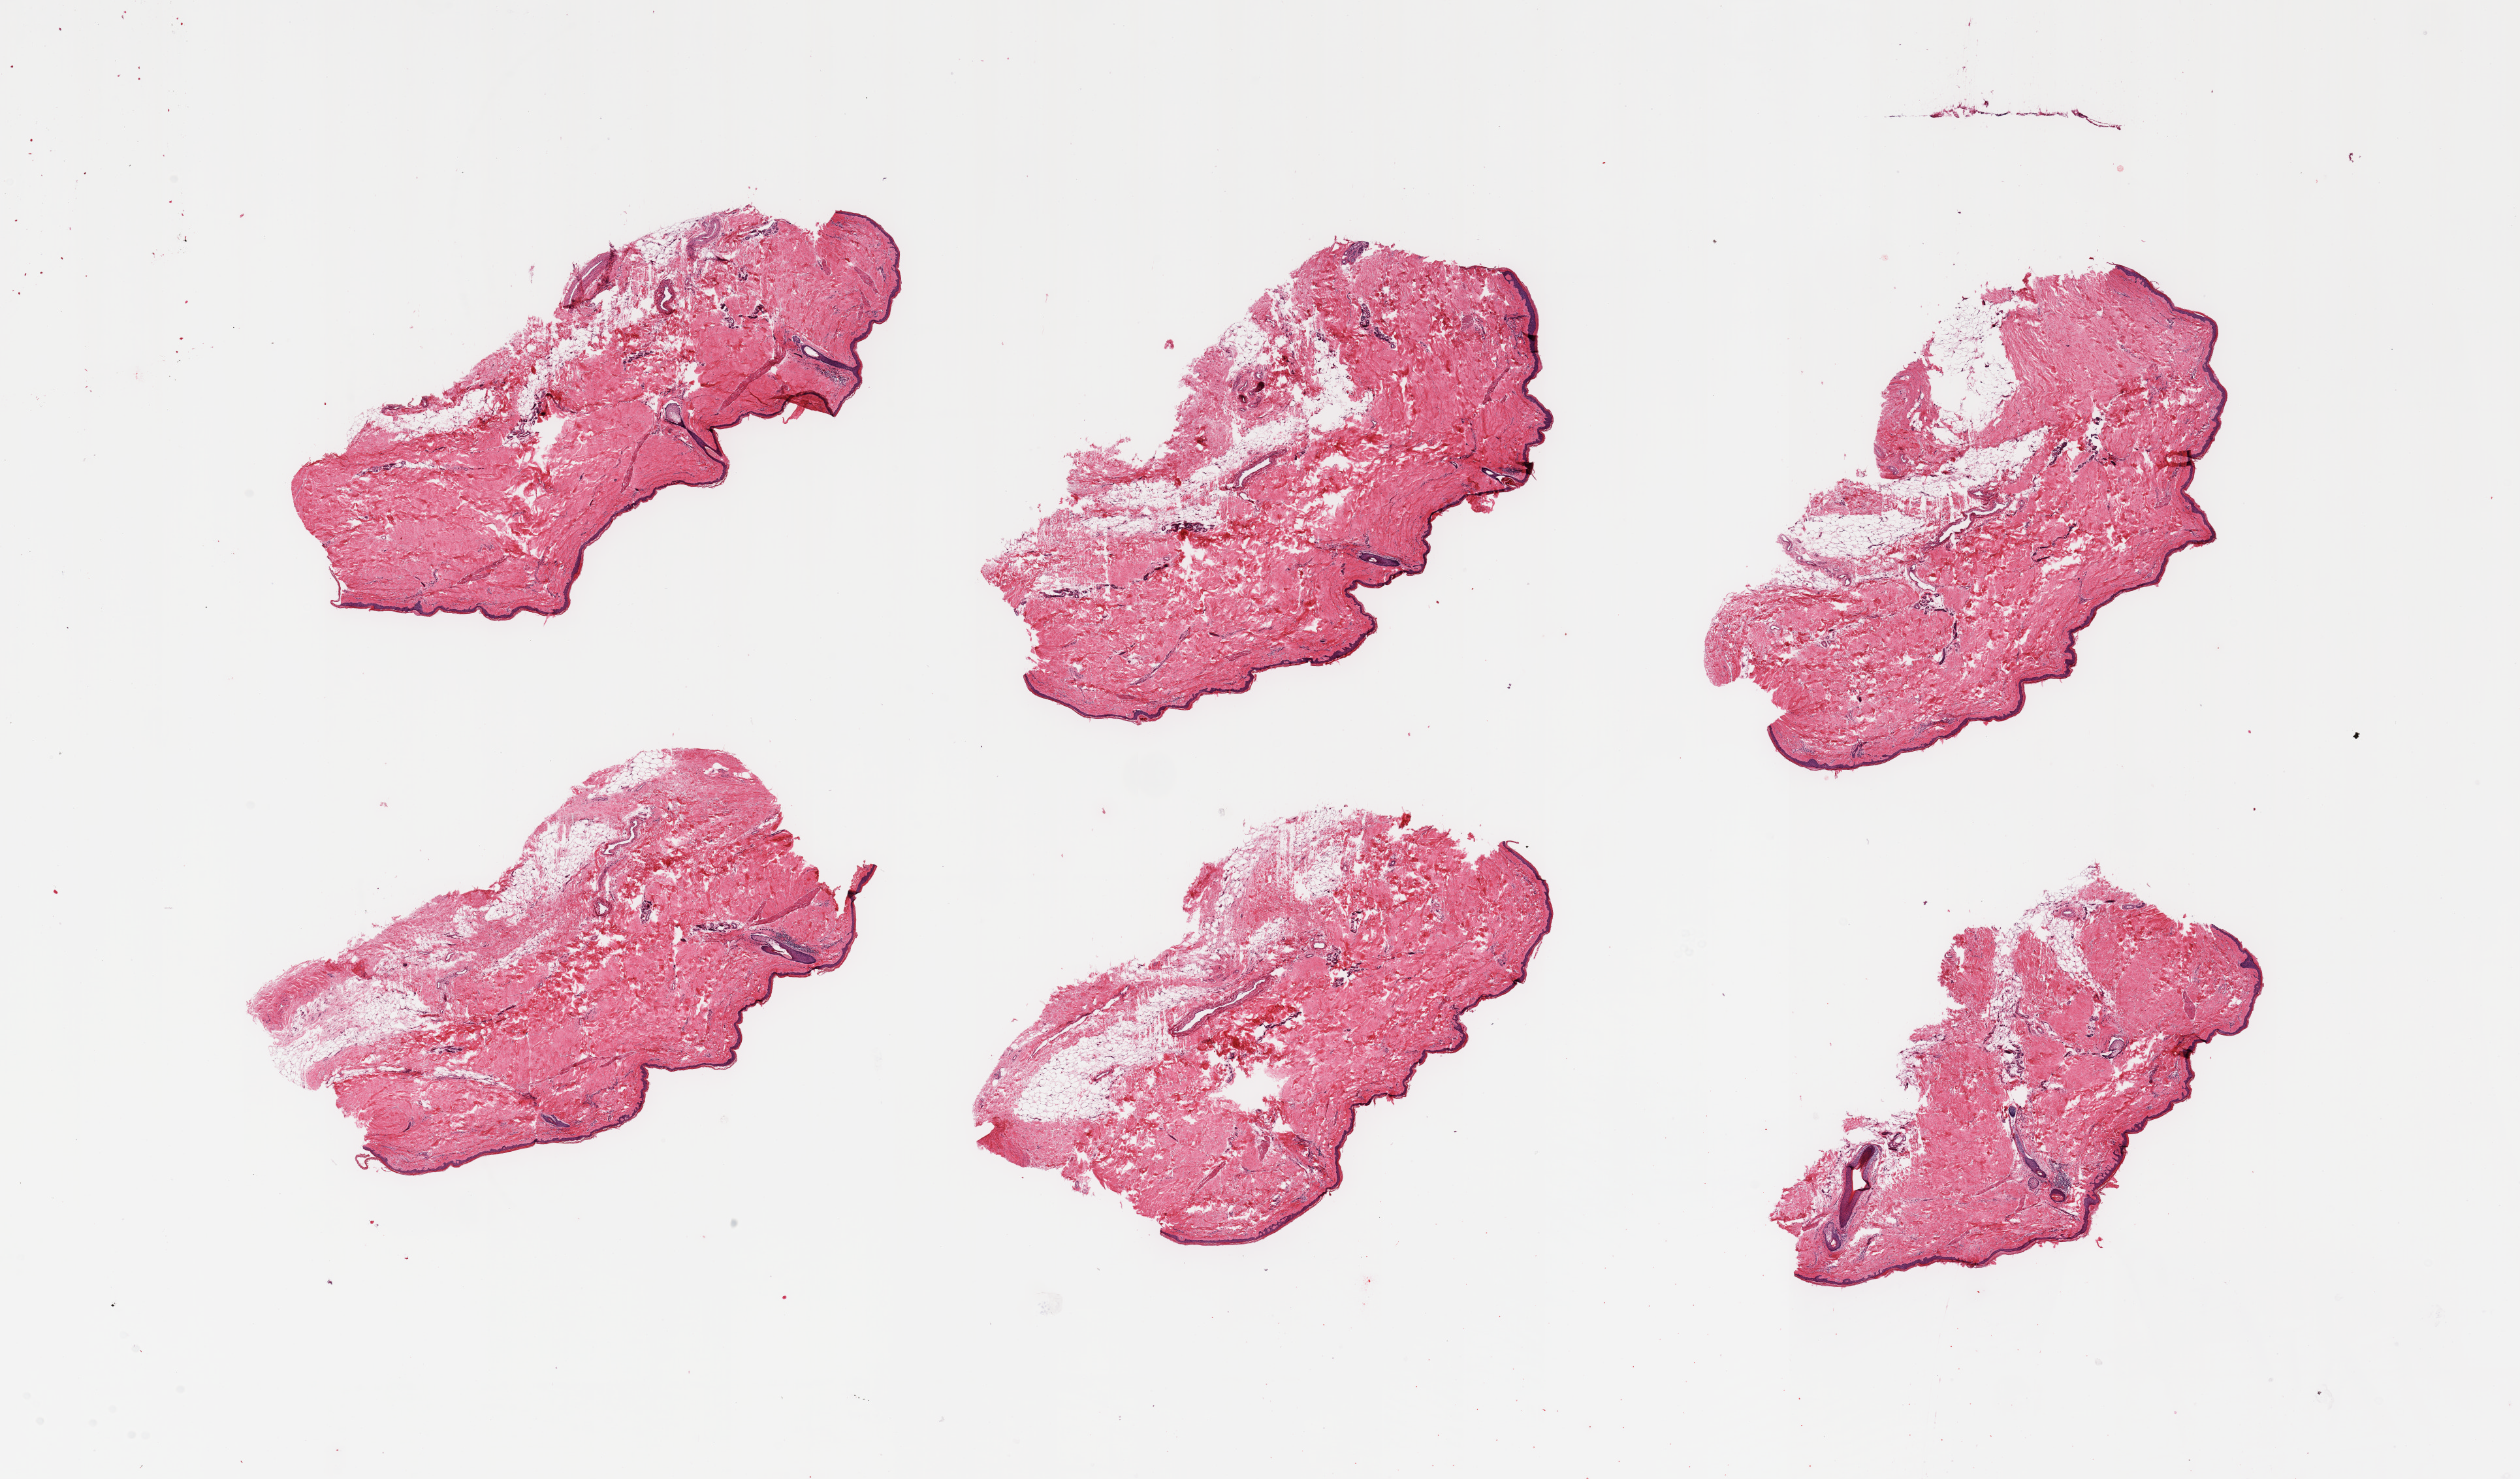
H&E whole-slide image — low-resolution overview of the scanned area, about 30.5 x 17.9 mm; PAXgene-fixed, paraffin-embedded tissue; sampled site (target tissue): skin of lower leg; tissue donor sample. Male donor.
Reviewer comment on this tissue sample: 6 pieces; 20% dermal fat; well trimmed.